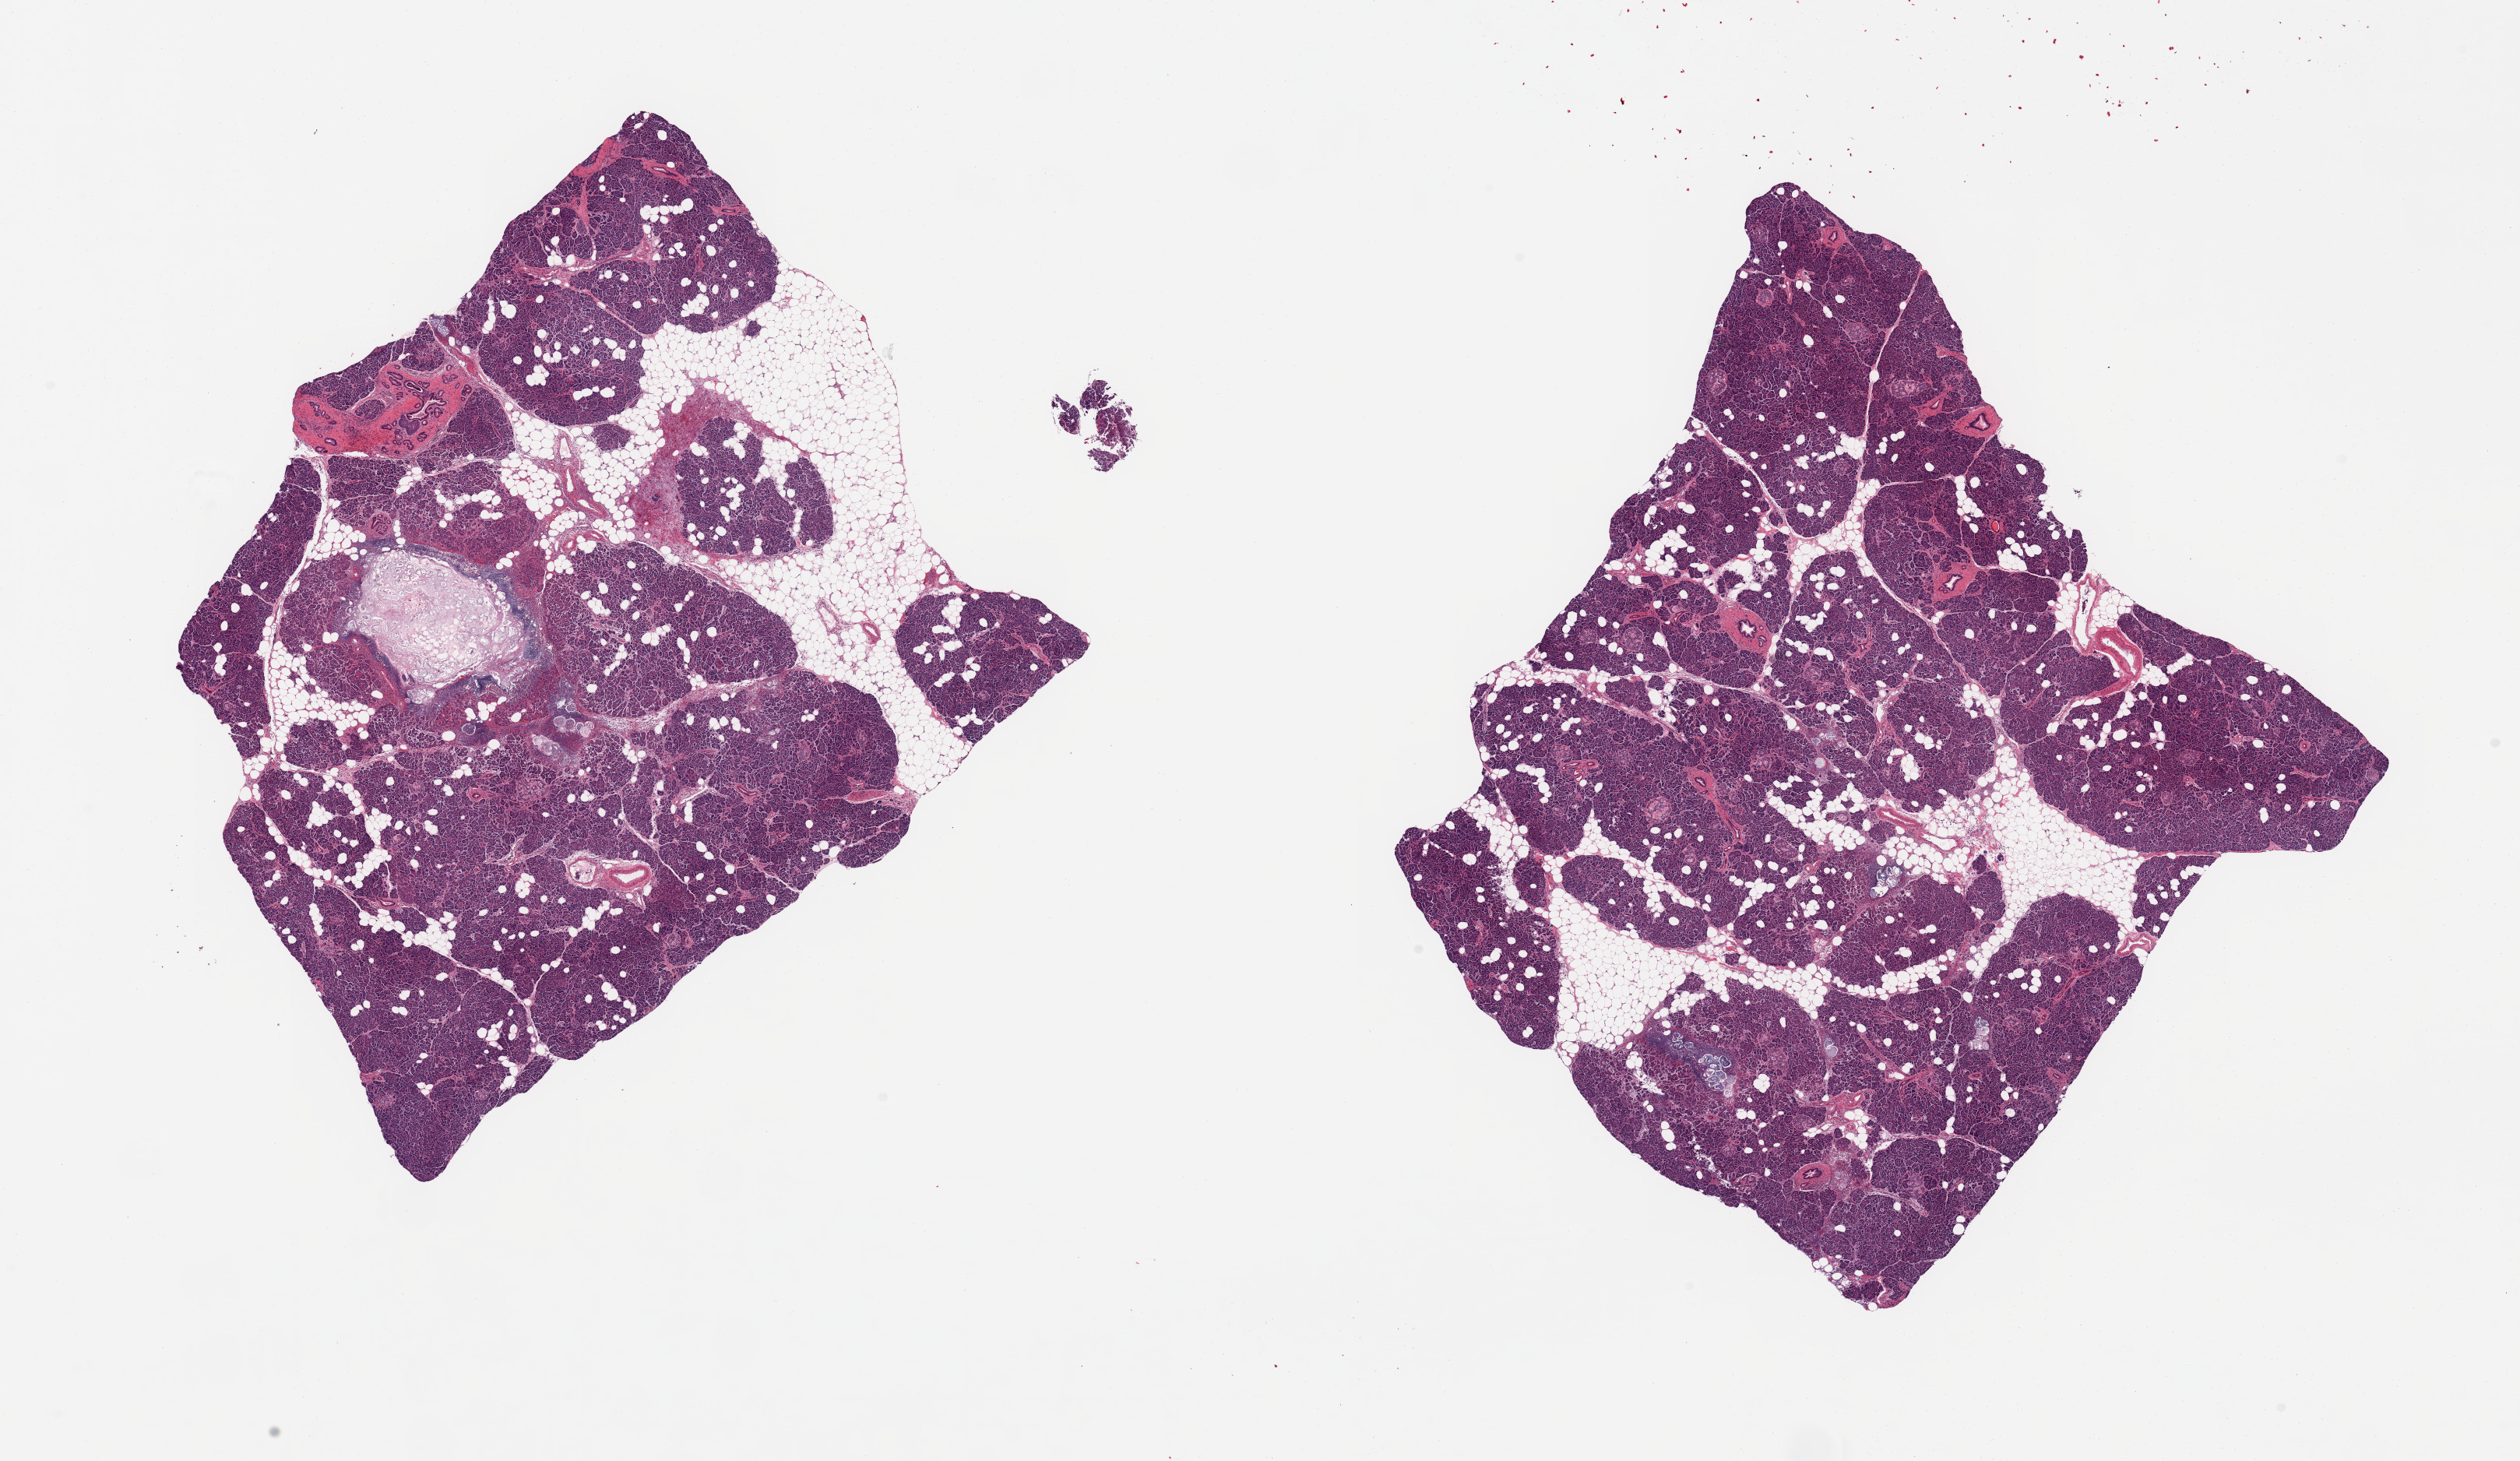
Digitized haematoxylin and eosin-stained section, brightfield — shown as a low-resolution overview of the whole scanned area (about 25.6 x 14.8 mm, slide scanned at 20x); PAXgene-fixed, paraffin-embedded tissue; target tissue: pancreas; tissue donor sample.
Pathologist's review note for this sample: 2 pieces; large [2.4mm] and smaller foci of pancreatic necrosis surrounded by a rim of leucocytes: acute pancreatitis ( and); ~20% internal fat; prominent Langerhans islets and some hyalinized.